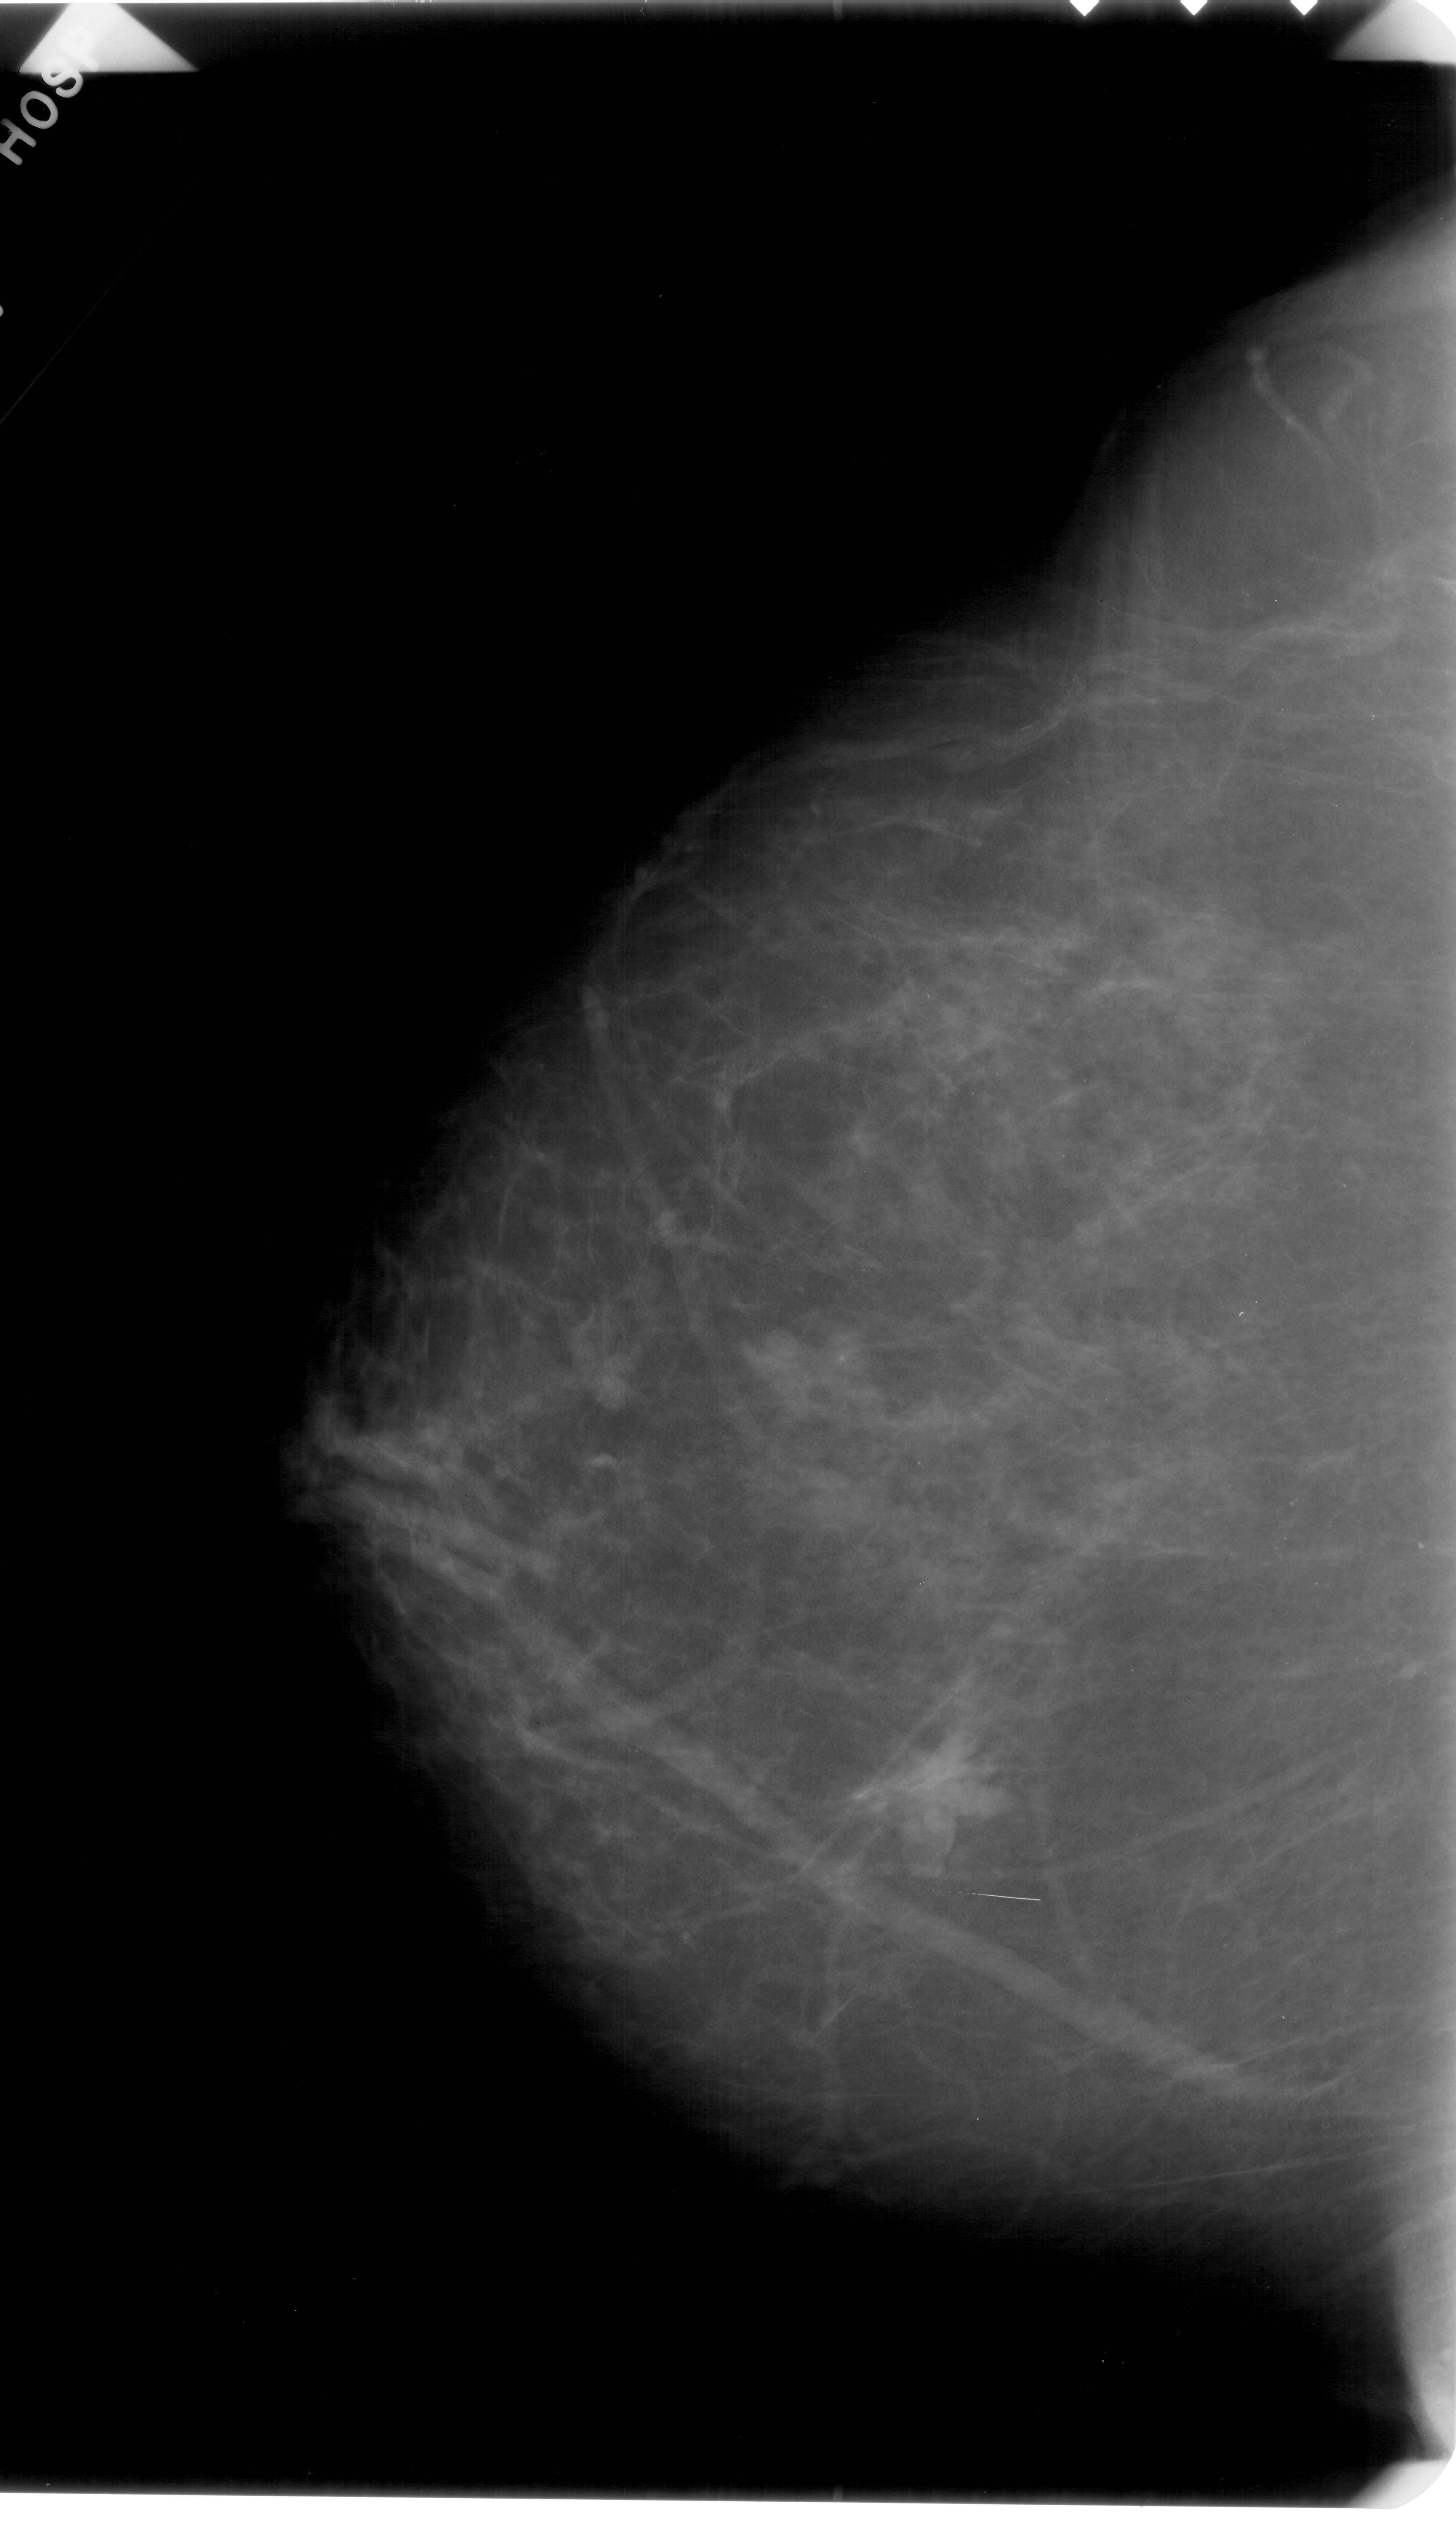
Scanned film-screen mammogram; left breast; CC view; breast composition: scattered fibroglandular densities (BI-RADS density category 2 of 4).
- Radiologist-marked abnormalities on this image: mass, shape irregular, margins ill defined; BI-RADS assessment category 4; subtlety rating 4 on a 1 (subtle) to 5 (obvious) scale; pathology result (as recorded, not read from the image): malignant.